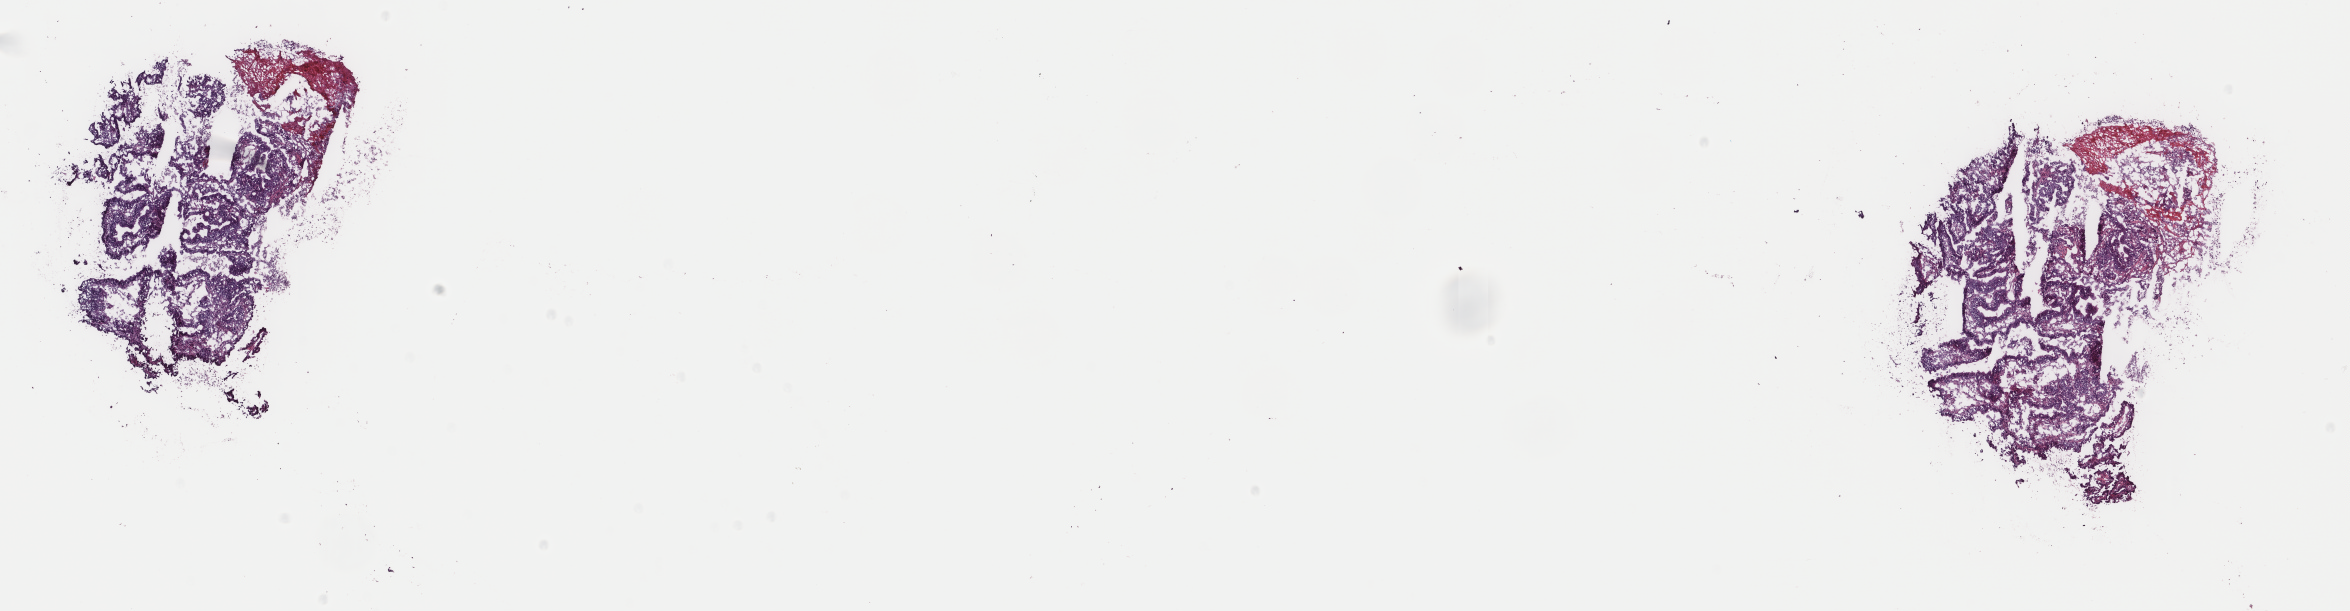
Whole-slide histology image, Hematoxylin and eosin (H&E) stained, shown as a low-resolution overview of the whole scanned area (about 18.7 x 4.8 mm); frozen section from the top of the tissue portion; sample: primary tumour, esophagus. Male patient; age at initial diagnosis 77 years. Histologic grade: G2 (moderately differentiated). Slide review estimates, as recorded: tumour cells 70%, tumour nuclei 90%, normal cells 20%, stromal cells 10%, necrosis 0%. Inflammatory infiltration, as recorded: lymphocyte infiltration 0%, monocyte infiltration 0%, neutrophil infiltration 0%.
- TNM: T1 N0 M0
- AJCC pathologic stage: I
- pathologic diagnosis: Adenocarcinoma, NOS (lower third of esophagus)
- lymph nodes positive (case pathology): 0 of 24 examined